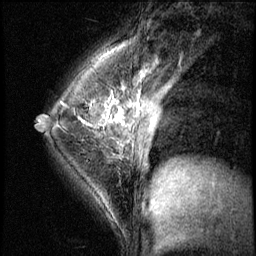
Breast MRI (dynamic contrast-enhanced), one sagittal slice; position 39 of 56 along the scan axis; 3 images stored at this slice position (order not interpretable as contrast timing); 1.5 T; TE 4.2 ms, TR 8.7 ms; 256 × 256 image matrix. Female patient, age 35 years. Case-level facts recorded for this patient, not image findings: setting: breast cancer imaged before/during neoadjuvant chemotherapy; receptor status: HER2-positive.
Outlined on this slice (semi-automatic segmentation, software-assisted and operator-edited):
- analysis volume of interest (the breast-tissue region the enhancement analysis was run in; not a lesion): bounding box (x1, y1, x2, y2) in pixels: (58, 84, 138, 186)
- tumour enhancement mask (voxels above the 140 % enhancement threshold inside the analysis volume of interest): (62, 103, 93, 126)